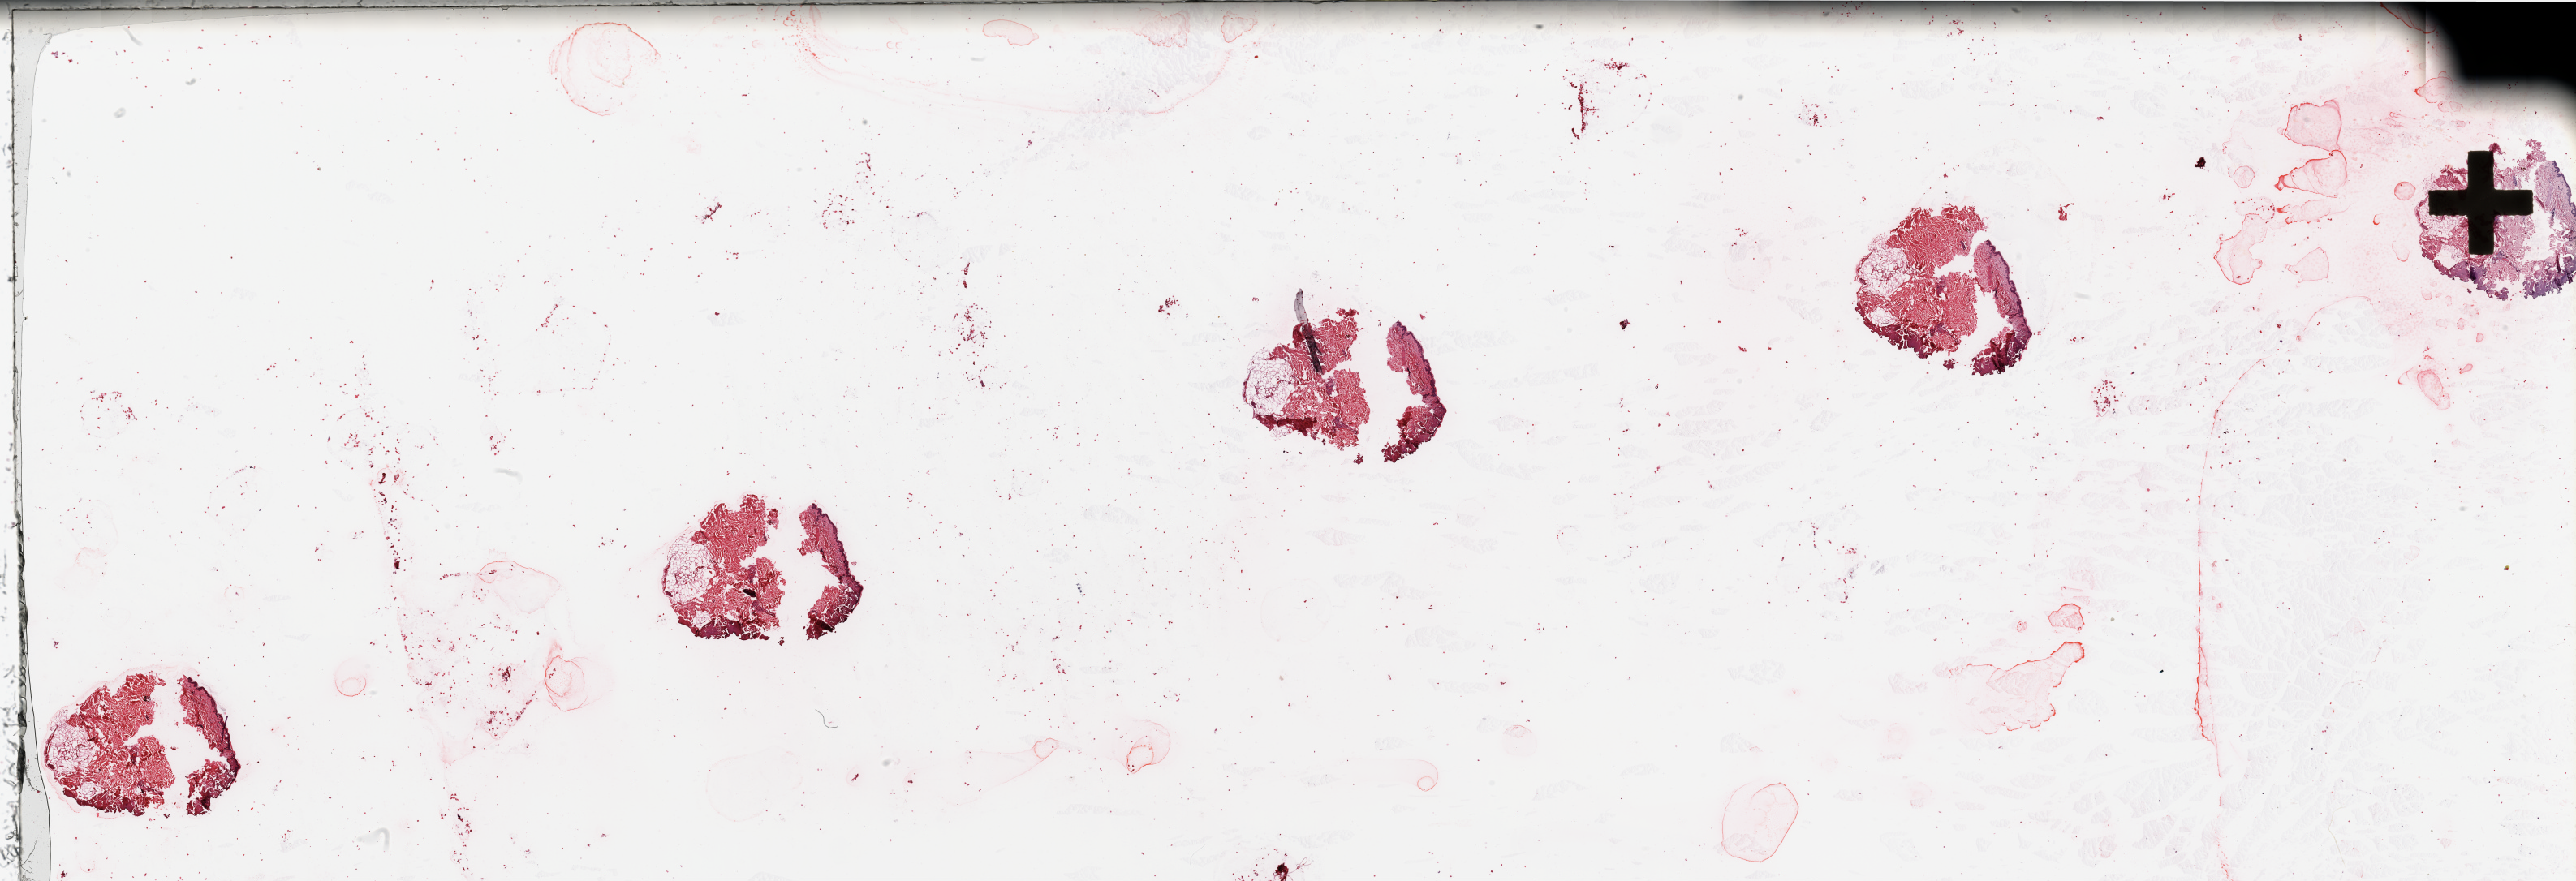
H&E whole-slide image — shown as a low-resolution overview of the whole scanned area (about 50.2 x 17.2 mm, slide scanned at 20x), normal (non-tumour) tissue sample, sampled site: trunk. Male, 69 y/o.
- this section: normal (non-tumour) tissue from the same patient
- patient diagnosis: Malignant melanoma, NOS